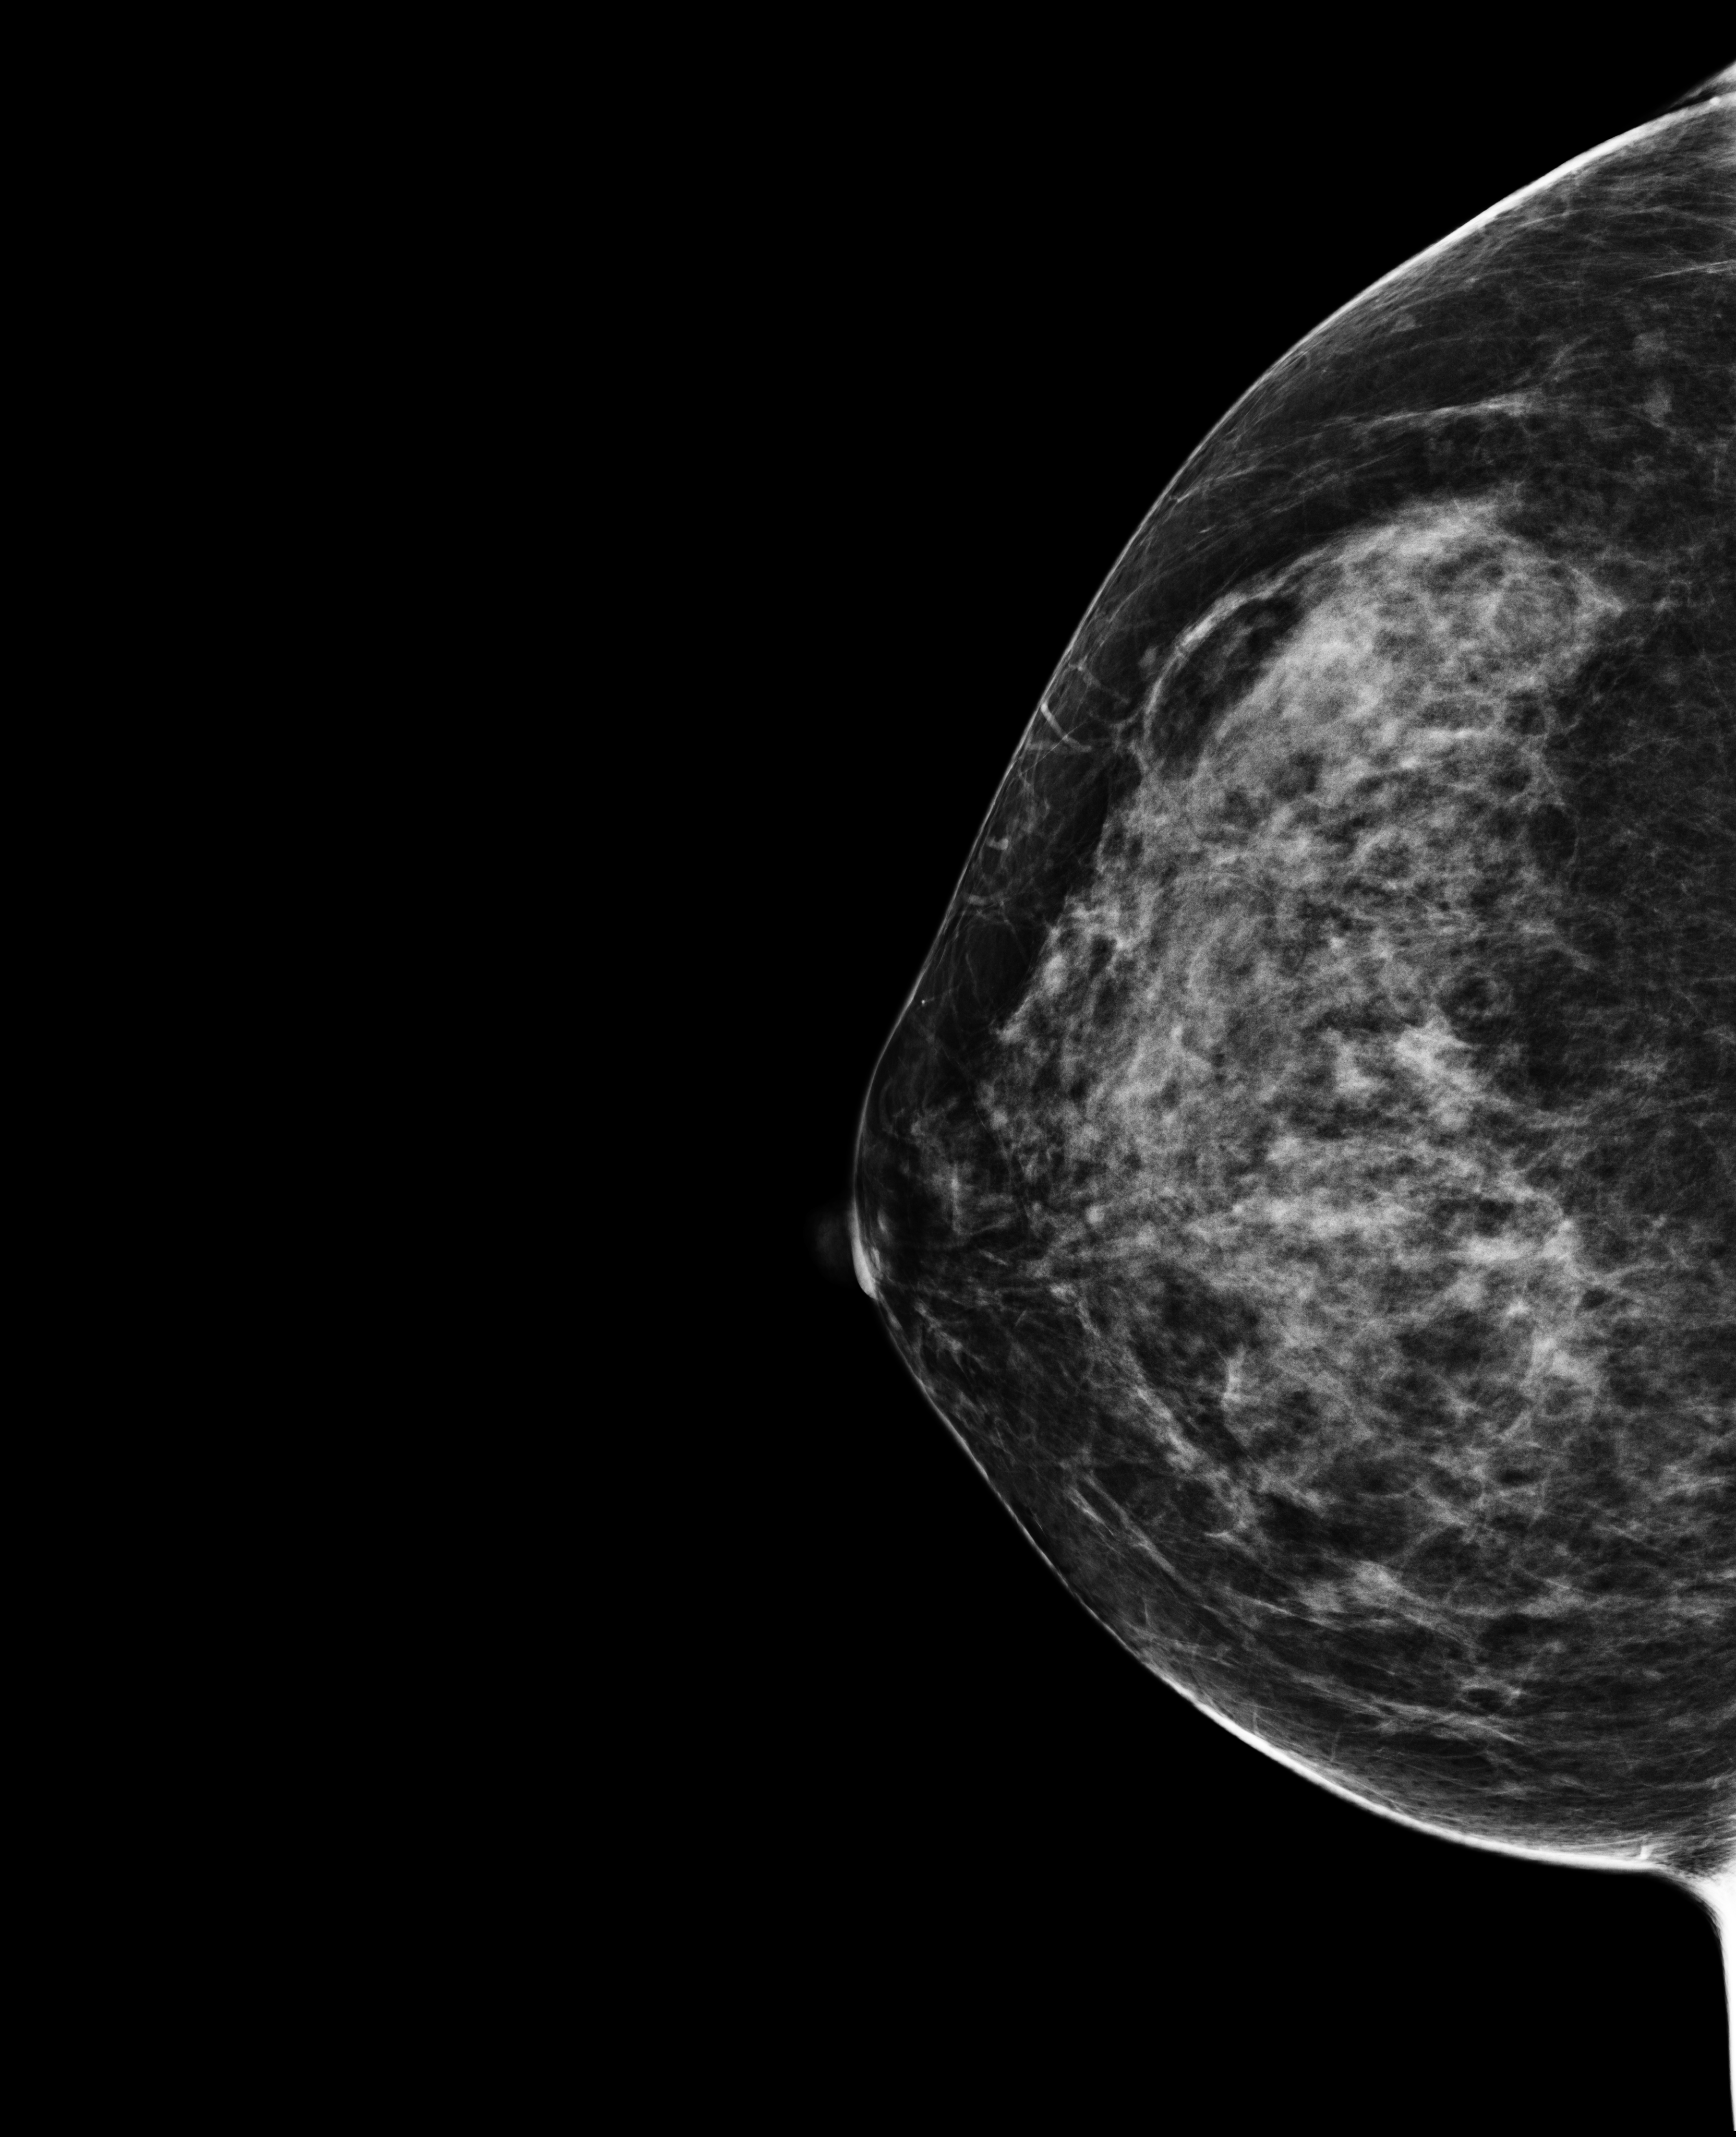
Screening examination; compressed breast thickness 63 mm. Female patient, age 47 years.
Image type: full-field digital mammogram. Breast: right. Projection: cranio-caudal projection.